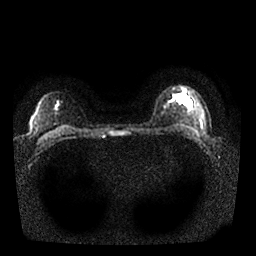
Breast MRI, one axial slice; position 19 of 25 along the scan axis; diffusion-weighted series; image 2 of 4 stored at this slice position (different b-values; order by instance number); 1.5 T; 4 mm slice thickness; 256 × 256 image matrix. Female patient.
Annotated regions visible in this slice (expert manual segmentation):
- tumour on diffusion-weighted imaging: box from (x=178, y=94) to (x=192, y=105) px